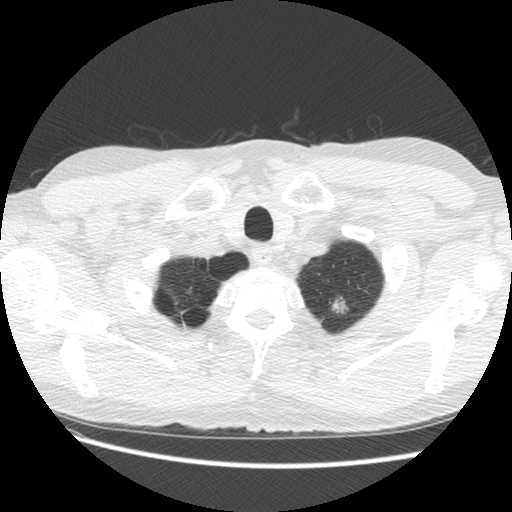
Low-dose screening chest CT, one axial slice; slice 117 of 131 in the series (ordered by position); lung window (W 1500 / L -600 HU); 2.5 mm slice thickness; 512 × 512 image matrix, field of view 340 × 340 mm.
Structures marked on this image (outlined manually by an expert reader):
- lesion 1 (tumor, upper lobe of left lung): box from (x=332, y=297) to (x=349, y=314) px